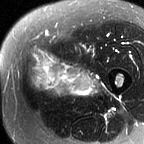
MRI of an extremity soft-tissue mass, one axial slice. Position 20 of 60 along the scan axis. T2-weighted fat-saturated. MR volume resampled by the dataset authors to the PET/CT grid (not the native acquisition matrix). 3.27 mm slice thickness. 144 × 144 image matrix. Female patient. From the clinical record (not read from this slice): histological type: pleiomorphic leiomyosarcoma; grade: intermediate; site of the primary tumour: left thigh.
Outlined on this slice (expert contour drawn on MRI and transferred to this co-registered scan by the dataset authors):
- gross tumour volume including surrounding oedema: bounding box [x1, y1, x2, y2] px = [27, 51, 105, 98]
- gross tumour volume (mass): [29, 53, 90, 98]